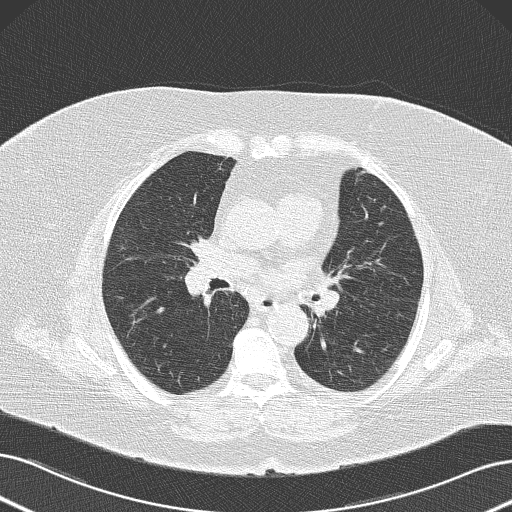
Chest CT (low-dose screening protocol), one axial image, first (baseline) screen, lung window (W 1500 / L -600 HU), 2 mm slice thickness, lung (sharp) reconstruction kernel (B50f), 120 kVp, slice 71 of 145 in the series, 512 × 512 image matrix, field of view 364 × 364 mm. Female, age 73 years at enrolment. Former smoker at enrolment.
Expert-annotated lung lesion, bounding box <97,216,145,263> (left, top, right, bottom; pixels). Reader record for this screening exam (exam-level; its link to the box is not recorded): non-calcified nodule or mass ≥4 mm, right upper lobe, 15 × 11 mm, poorly defined margins, soft tissue attenuation. Official screen result: positive, change unspecified: nodule(s) >= 4 mm or enlarging nodule(s), mass(es), or other non-specific abnormalities suspicious for lung cancer. Participant outcome: lung cancer diagnosed 55 days after this screen — neoplasm, malignant, right upper lobe, stage IA (AJCC 6th edition), 15 mm at pathology.